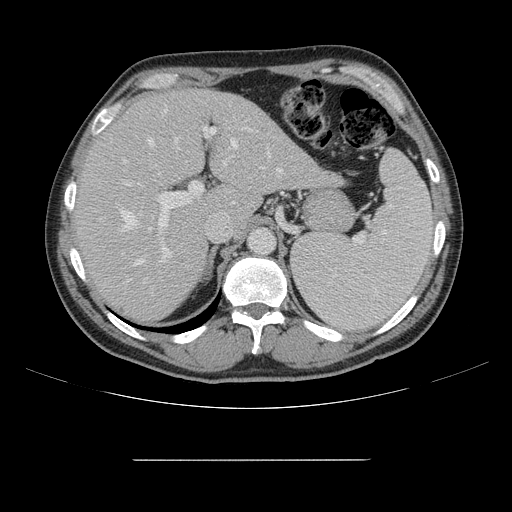
Contrast-enhanced abdominal CT, one axial slice; slice 105 of 164 in the series (ordered by position); 120 kVp; intravenous contrast given; soft-tissue window (W 400 / L 40 HU); 2.5 mm slice thickness; 512 × 512 image matrix, field of view 404 × 404 mm. Male patient, age 54 years. Case-level facts recorded for this patient, not image findings: diagnosis: colorectal cancer liver metastases, imaged before liver resection; multiple liver metastases: yes; largest metastasis: 1 cm; disease in both lobes: no.
Structures marked on this image (manually delineated by an expert):
- hepatic veins: bounding box [x1, y1, x2, y2] px = [121, 139, 283, 266]
- liver: [76, 89, 338, 323]
- planned liver remnant (the part of the liver to remain after resection): [76, 89, 239, 322]
- portal vein (with intrahepatic branches): [120, 106, 217, 296]